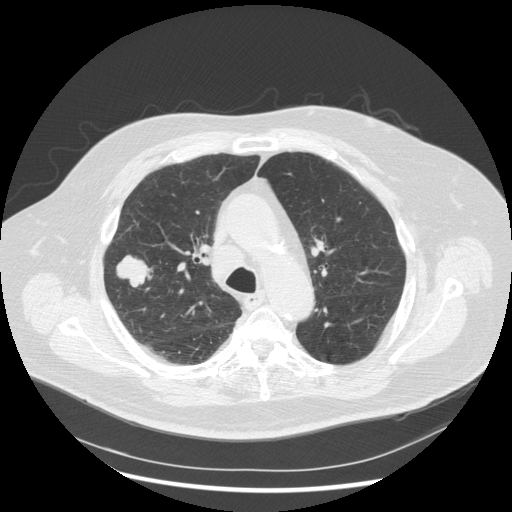
Chest CT (low-dose screening protocol), one axial image, third annual screen, lung window (W 1500 / L -600 HU), 2.5 mm slice thickness, standard (soft-tissue) reconstruction kernel (STANDARD). Male participant, aged 72 years at enrolment.
Lesion marked by an expert reader, bounding box [x1, y1, x2, y2] px = [103, 250, 158, 298]. The exam's reader record, not a measurement of the box and not confirmed to be the same lesion: non-calcified nodule or mass ≥4 mm, right upper lobe, 31 × 31 mm, poorly defined margins, soft tissue attenuation, pre-existing on the prior screen: no. Participant outcome: lung cancer diagnosed 70 days after this screen — squamous cell carcinoma, NOS, right upper lobe, poorly differentiated (G3), stage IIIA (AJCC 6th edition), 19 mm at pathology.